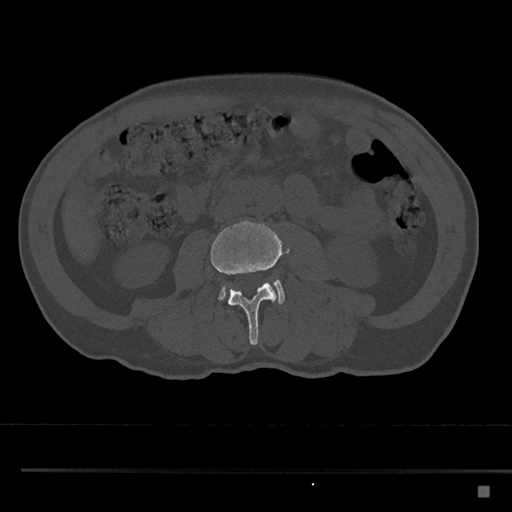
CT including the spine, one axial slice; position 682 of 797 along the scan axis; bone window (W 1800 / L 400 HU); 0.5 mm slice thickness; 512 × 512 image matrix, field of view 391 × 391 mm. Patient: male, 59 years. From the clinical record (not read from this slice): primary cancer: prostate.
Structures marked on this image (semi-automatic segmentation, software-assisted and operator-edited):
- L3 vertebra: box from (x=210, y=220) to (x=285, y=345) px
- L4 vertebra: (x=218, y=279)–(x=286, y=305)